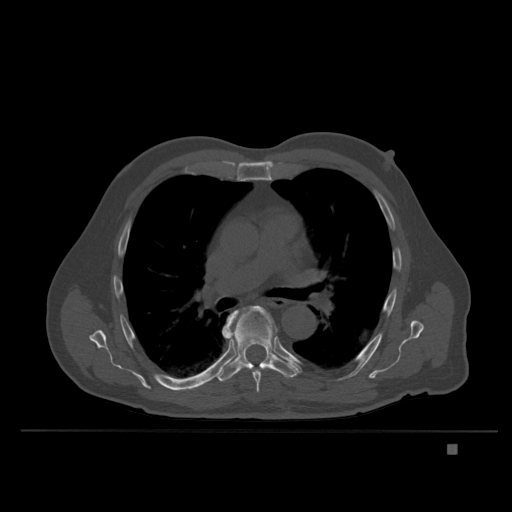
CT including the spine, one axial slice; position 250 of 435 along the scan axis; bone window (W 1800 / L 400 HU); 512 × 512 image matrix. Patient: male, 73 years. Case-level facts recorded for this patient, not image findings: primary cancer: skin.
Outlined on this slice (semi-automatically segmented with operator editing):
- T6 vertebra: bounding box <222,305,277,393> (left, top, right, bottom; pixels)
- T7 vertebra: <212,306,300,382>